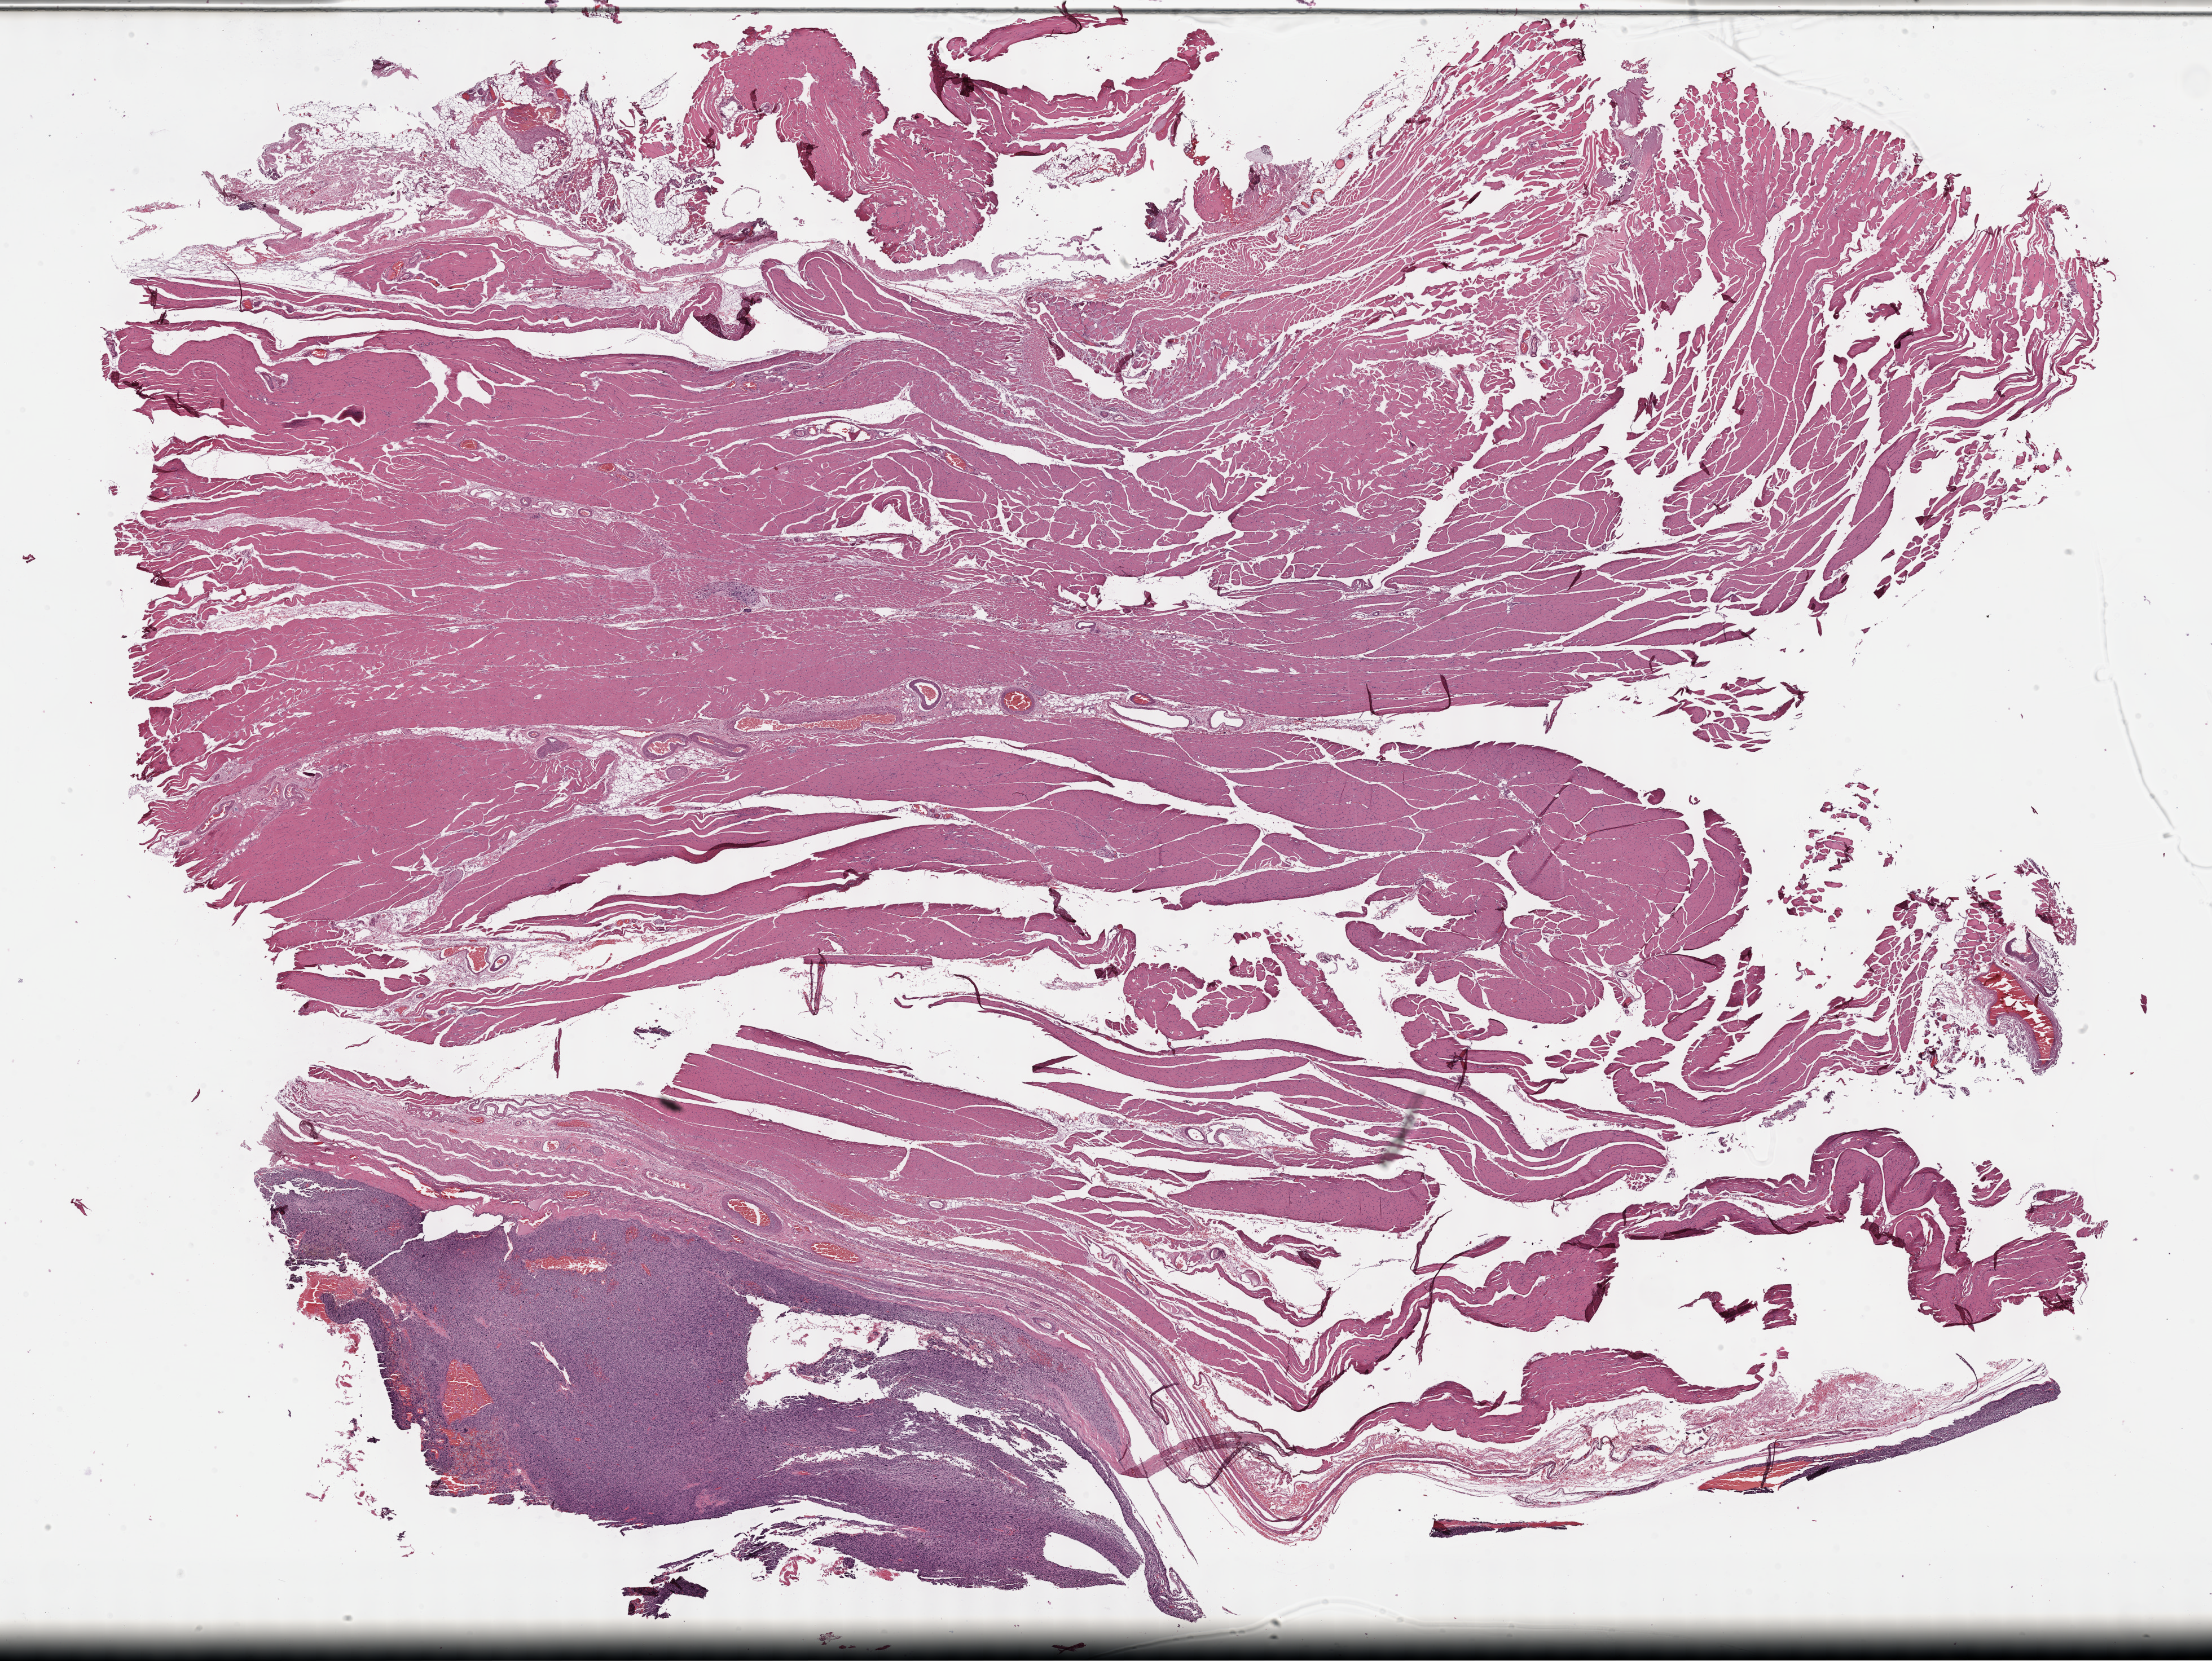
Hematoxylin and eosin (H&E) stained whole-slide image, low-resolution overview of the scanned area, about 31.7 x 23.8 mm. Formalin-fixed paraffin-embedded (FFPE) diagnostic section. Sample: primary tumour, connective, subcutaneous and other soft tissues. Patient: female, age at initial diagnosis 80 years.
• pathologic diagnosis: Undifferentiated sarcoma (connective, subcutaneous and other soft tissues of lower limb and hip)